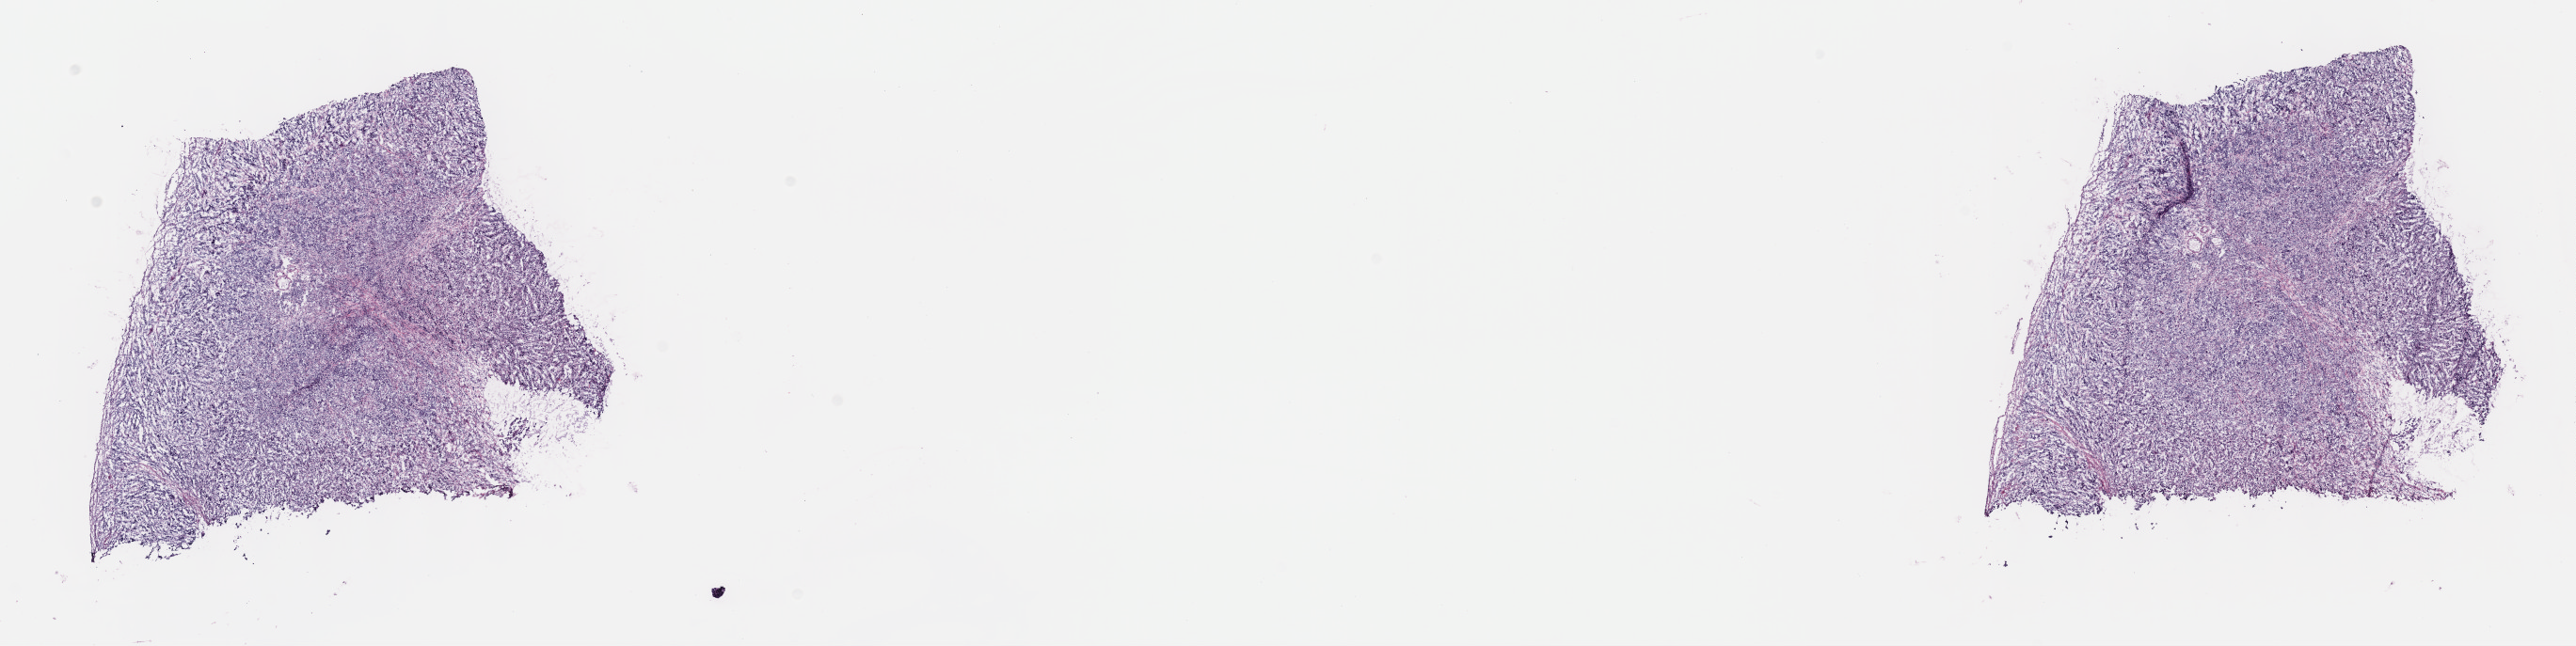
H&E-stained whole-slide image, low-resolution overview of the scanned area, about 22.1 x 5.6 mm. Frozen section from the top of the tissue portion. Primary tumour sample from the stomach. Male patient; age at initial diagnosis 82 years. Histologic grade: G3 (poorly differentiated). Slide review estimates, as recorded: tumour cells 65%, tumour nuclei 75%, normal cells 0%, stromal cells 15%, necrosis 20%. Inflammatory infiltration, as recorded: lymphocyte infiltration 18%, monocyte infiltration 3%, neutrophil infiltration 3%.
• histologic diagnosis: Carcinoma, diffuse type (fundus of stomach)
• AJCC pathologic stage: IB